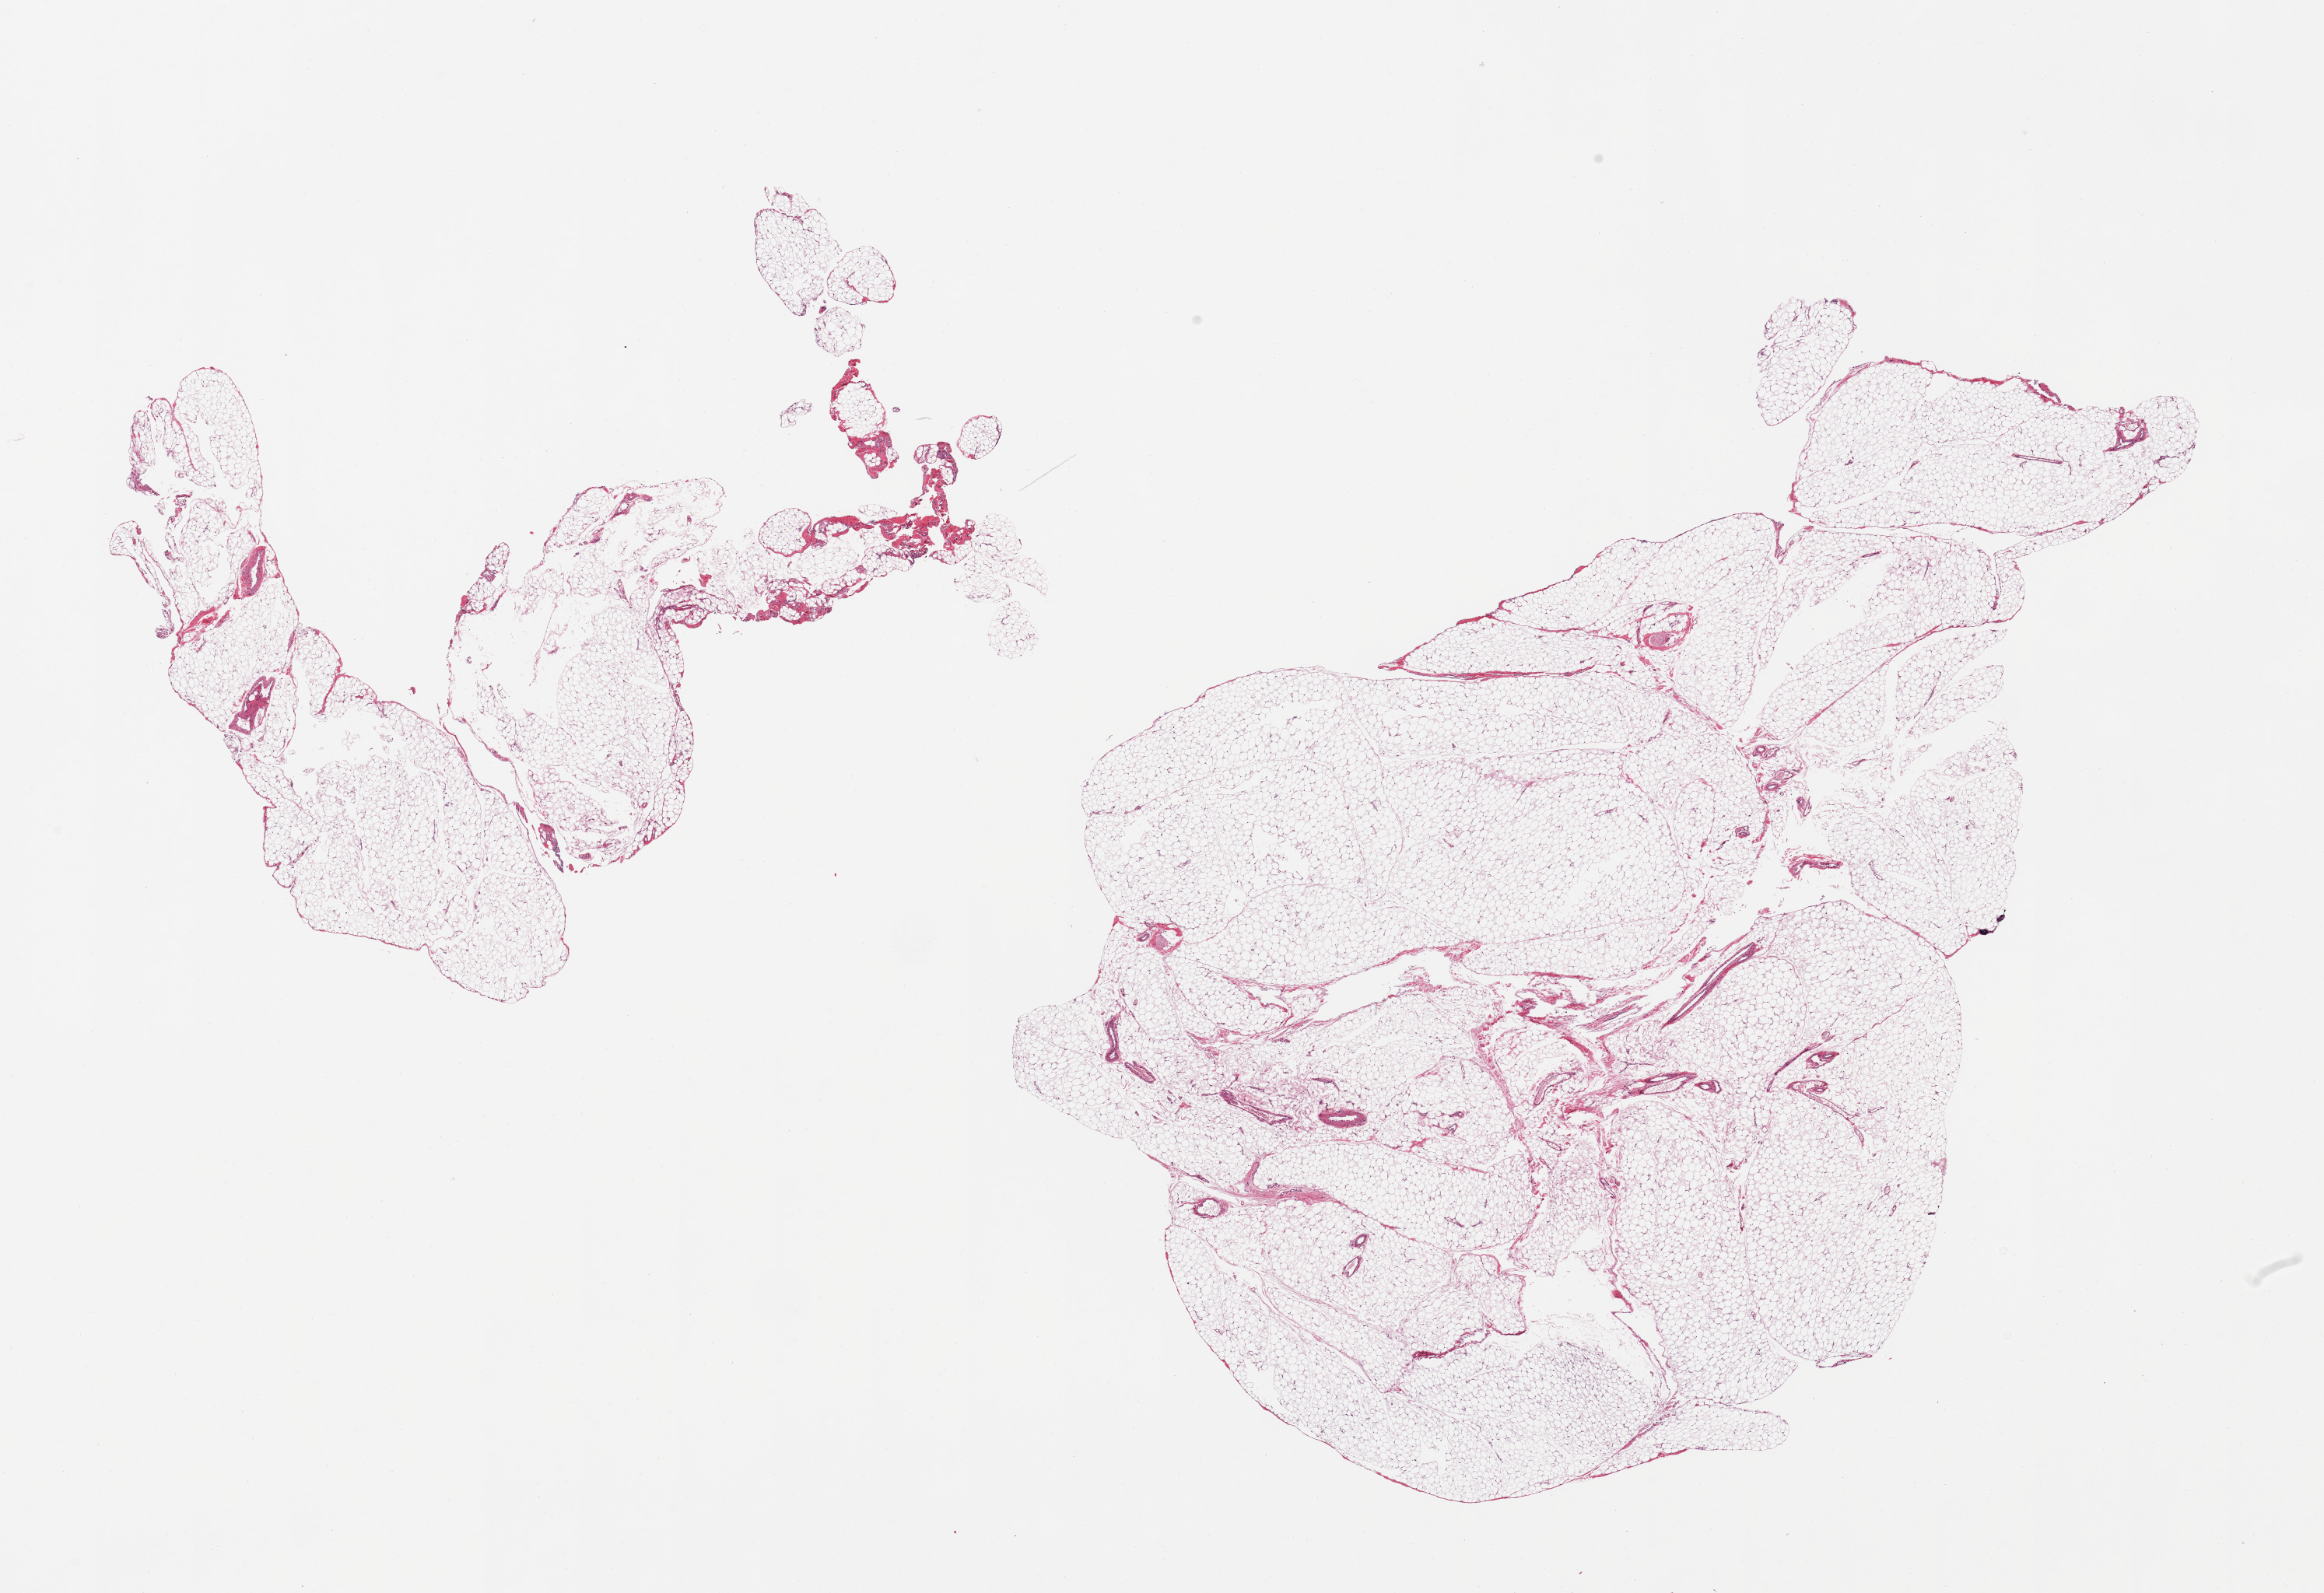
Whole-slide image, hematoxylin and eosin (H&E) stain, brightfield — whole scanned area (about 23.6 x 16.2 mm) shown as a low-resolution overview, PAXgene-fixed, paraffin-embedded tissue, sampled site (target tissue): omentum, tissue donor sample. Donor sex: male.
Pathologist's review note for this sample: 2 pieces, minimal fascia/vasular elements.